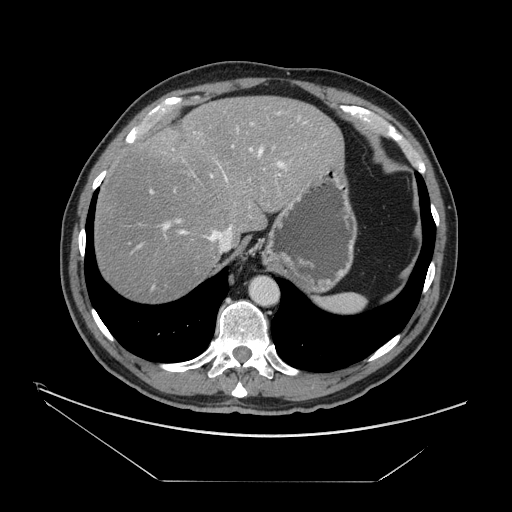
Contrast-enhanced abdominal CT, one axial slice. Position 123 of 161 along the scan axis. Reconstruction kernel STANDARD. 120 kVp. Intravenous contrast given. Soft-tissue window (W 400 / L 40 HU). 512 × 512 image matrix, field of view 440 × 440 mm. Male patient, age 65 years. From the clinical record (not read from this slice): diagnosis: colorectal cancer liver metastases, imaged before liver resection; multiple liver metastases: yes; largest metastasis: 4.2 cm; disease in both lobes: yes.
Outlined on this slice (outlined manually by an expert reader):
- hepatic veins: bounding box (x1, y1, x2, y2) in pixels: (177, 148, 263, 253)
- liver: (94, 96, 342, 303)
- planned liver remnant (the part of the liver to remain after resection): (94, 96, 342, 304)
- portal vein (with intrahepatic branches): (149, 111, 307, 230)
- liver metastasis: (175, 126, 184, 132)